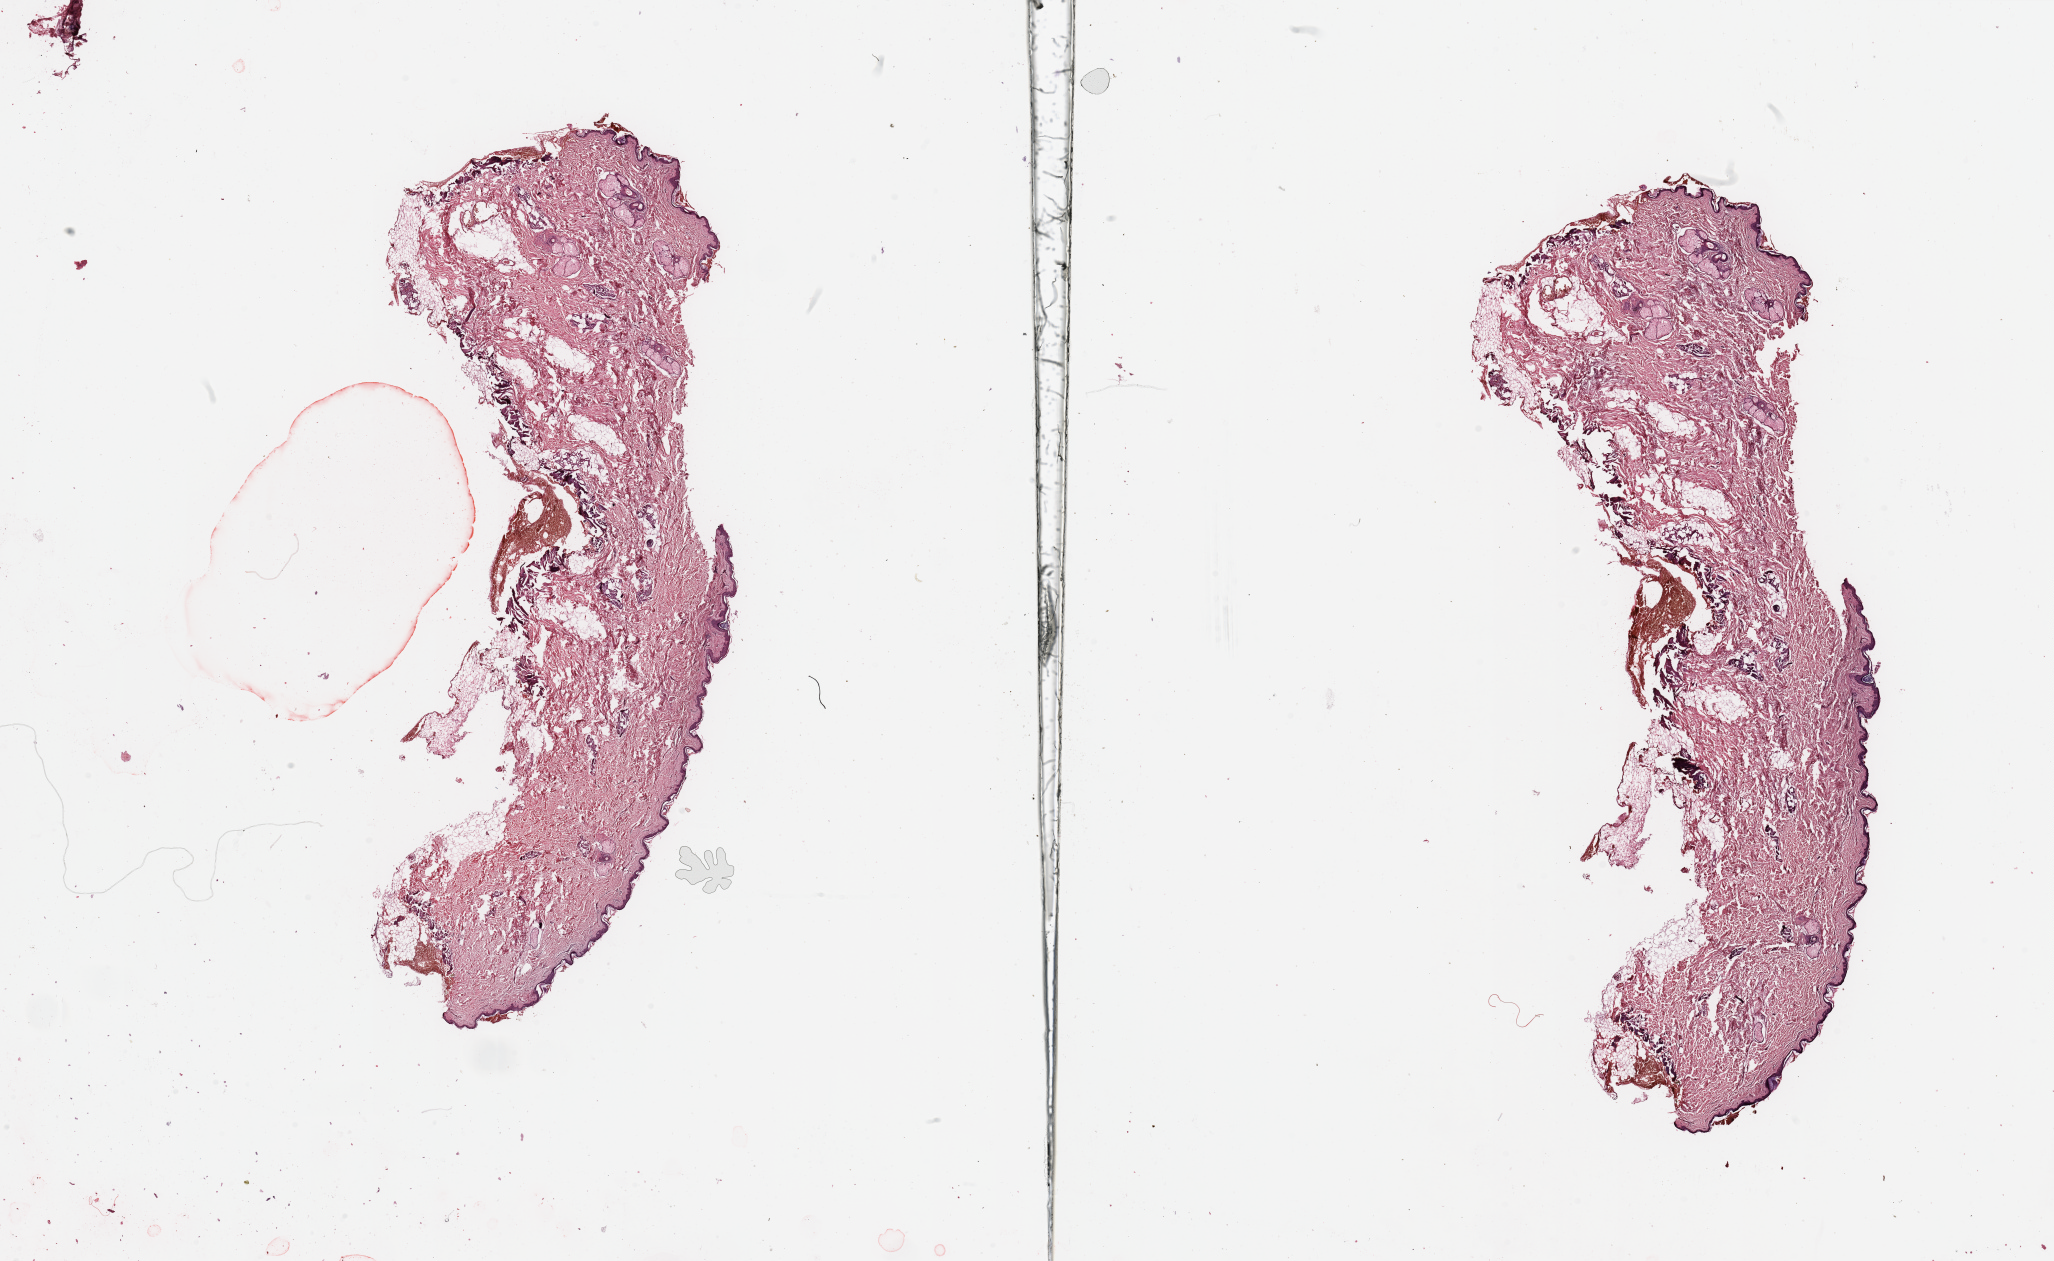
Whole-slide histology image, H&E, shown as a low-resolution overview of the whole scanned area (about 32.5 x 19.9 mm, slide scanned at 20x). Normal (non-tumour) tissue sample, sampled site: trunk. Patient: male, age 66 years.
* this section: normal (non-tumour) tissue from the same patient
* patient diagnosis: Malignant melanoma, NOS